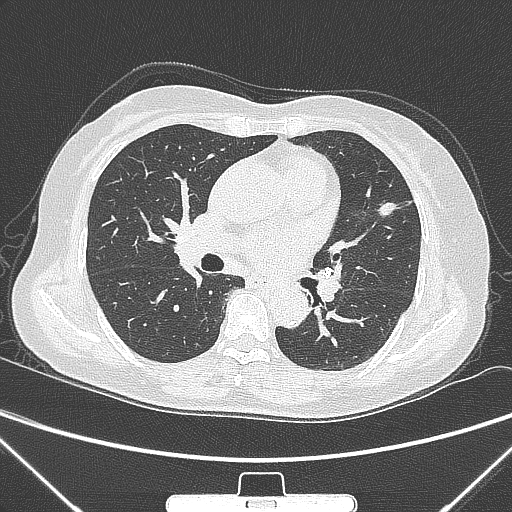
Chest CT, one axial slice; slice 150 of 300 in the series (ordered by position); 120 kVp; lung window (W 1500 / L -600 HU); 1 mm slice thickness; 512 × 512 image matrix. Female patient, age 70 years. Case-level facts recorded for this patient, not image findings: clinical TNM (as recorded): T1b N0 M0.
Outlined on this slice (bounding box drawn by a radiologist):
- lung tumour (recorded histology: adenocarcinoma): box from (x=368, y=190) to (x=398, y=231) px